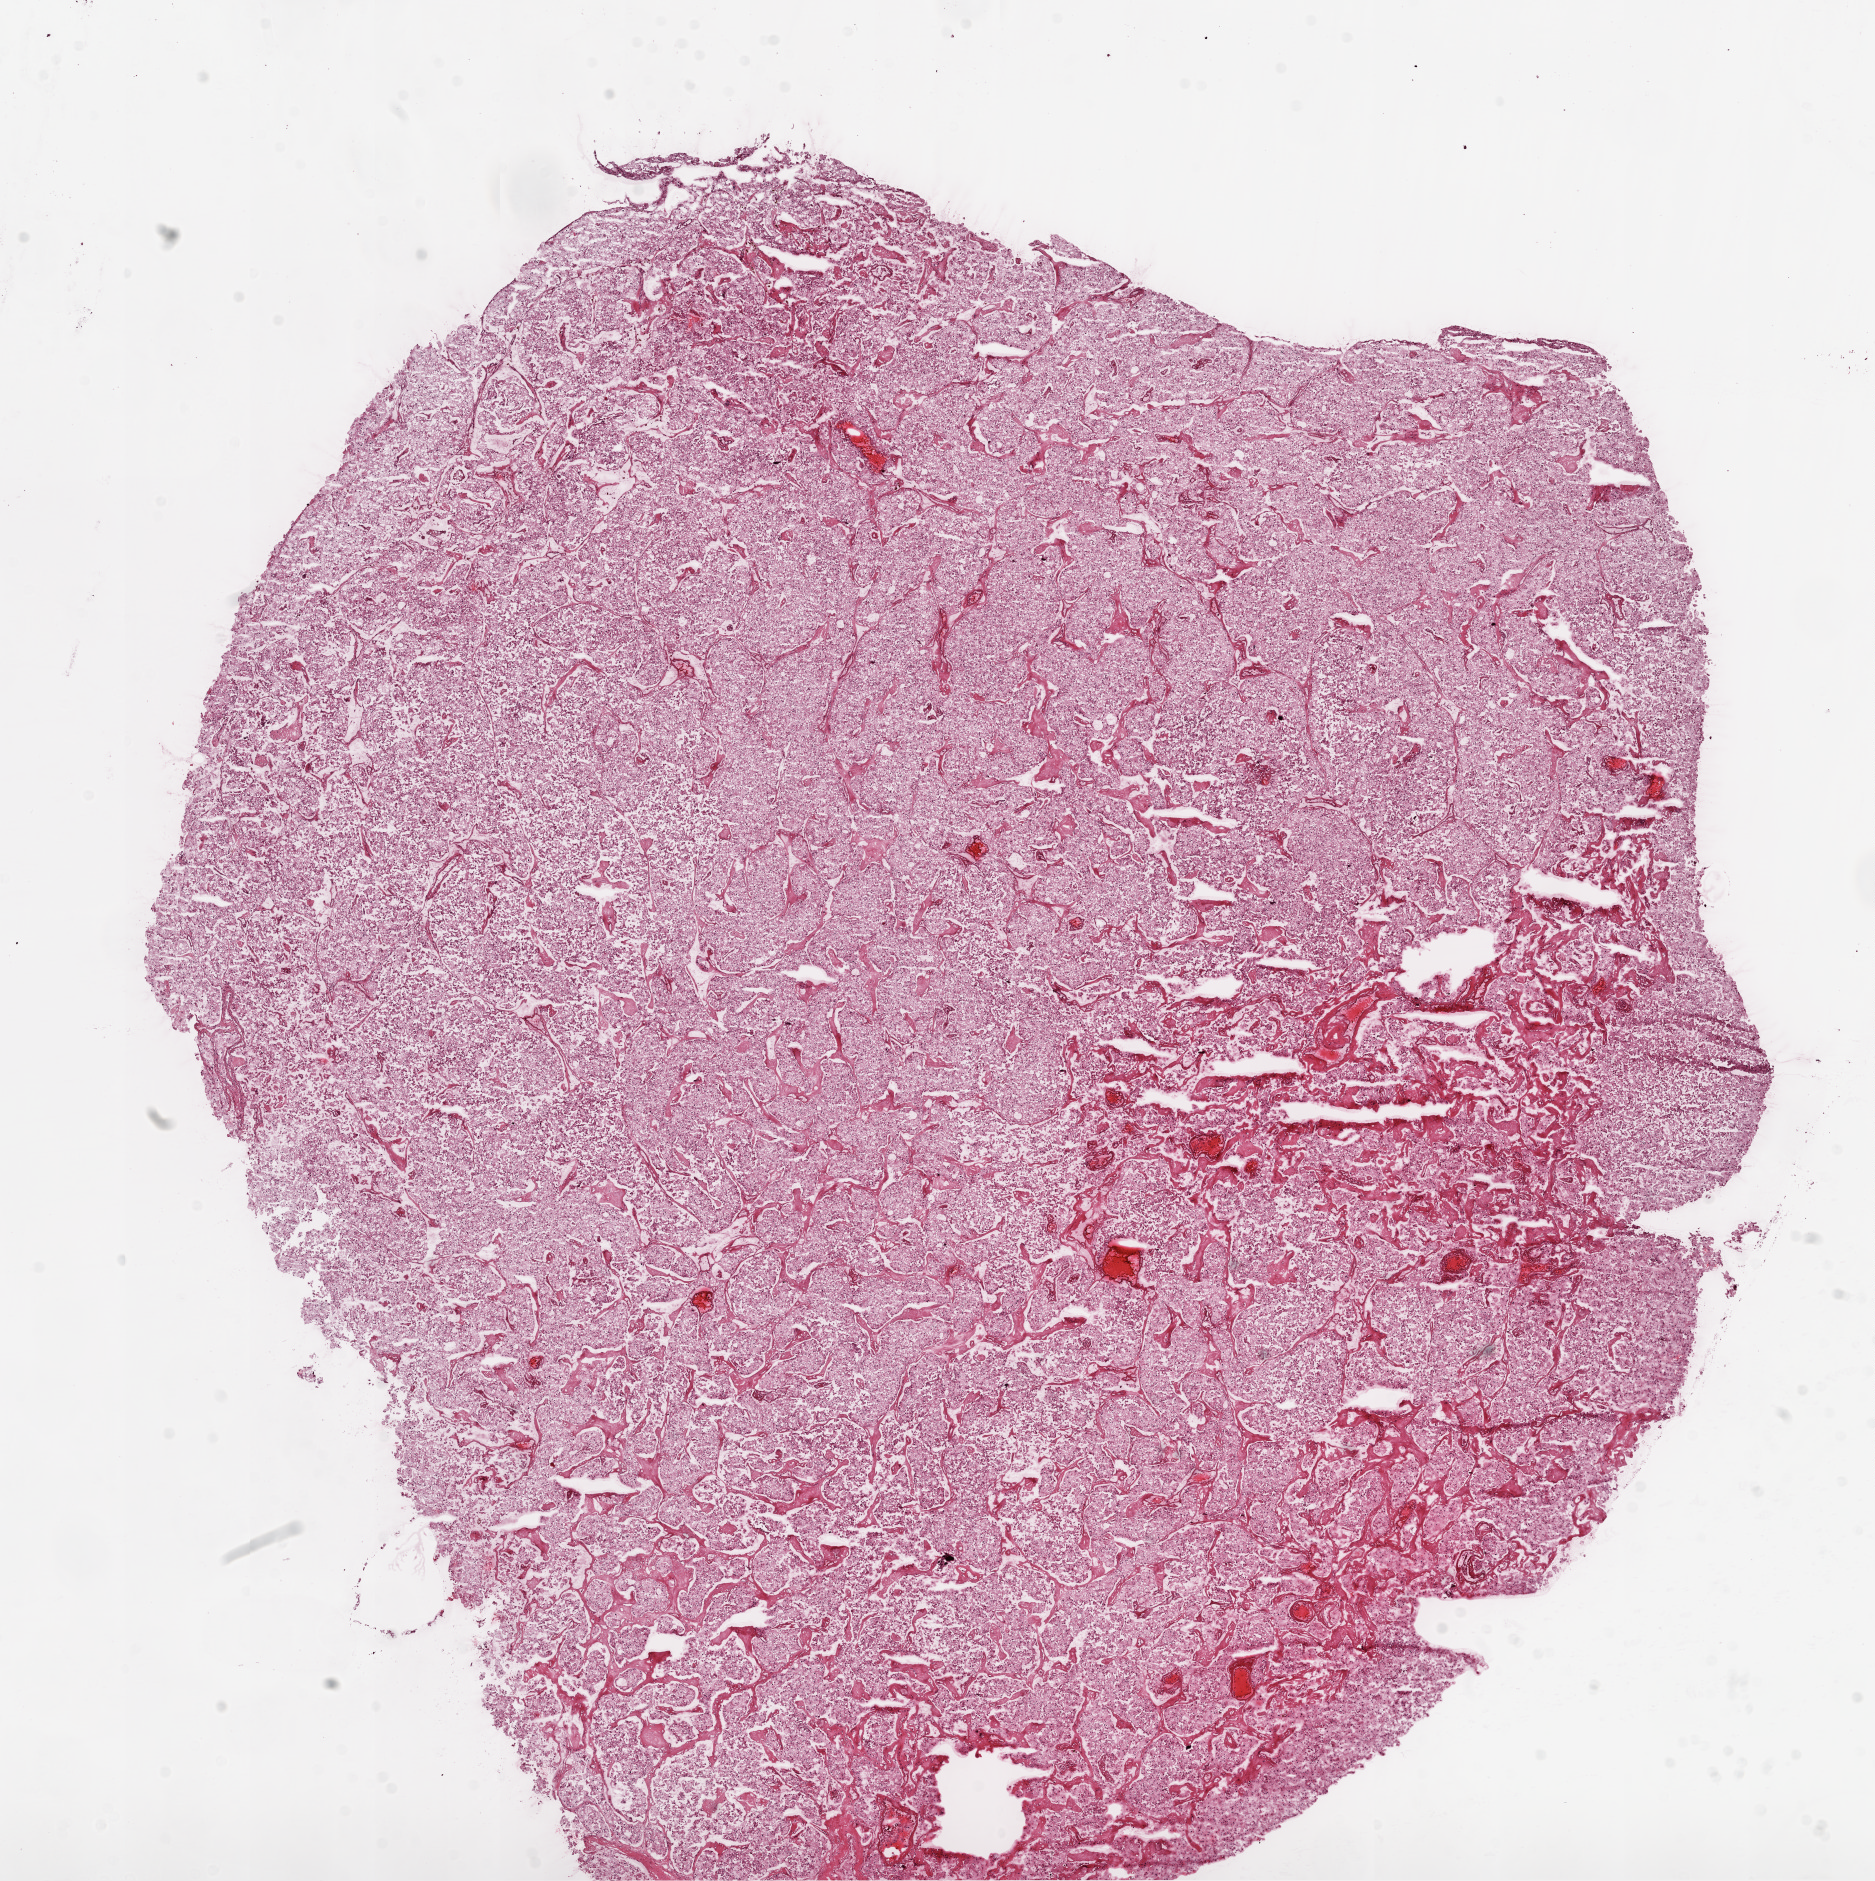
Digitized H&E tissue section (whole slide) — low-resolution overview of the scanned area, about 15.0 x 15.1 mm (slide scanned at 20x); frozen section from the top of the tissue portion; sample: primary tumour, kidney. Patient: male, age at initial diagnosis 56 years. Histologic grade: G3 (poorly differentiated). Pathologist review of this section (percent, as recorded): tumour cells 95%, tumour nuclei 80%, normal cells 0%, stromal cells 5%, necrosis 0%.
Diagnosis: Clear cell adenocarcinoma, NOS. AJCC pathologic stage: III. Laterality: right.